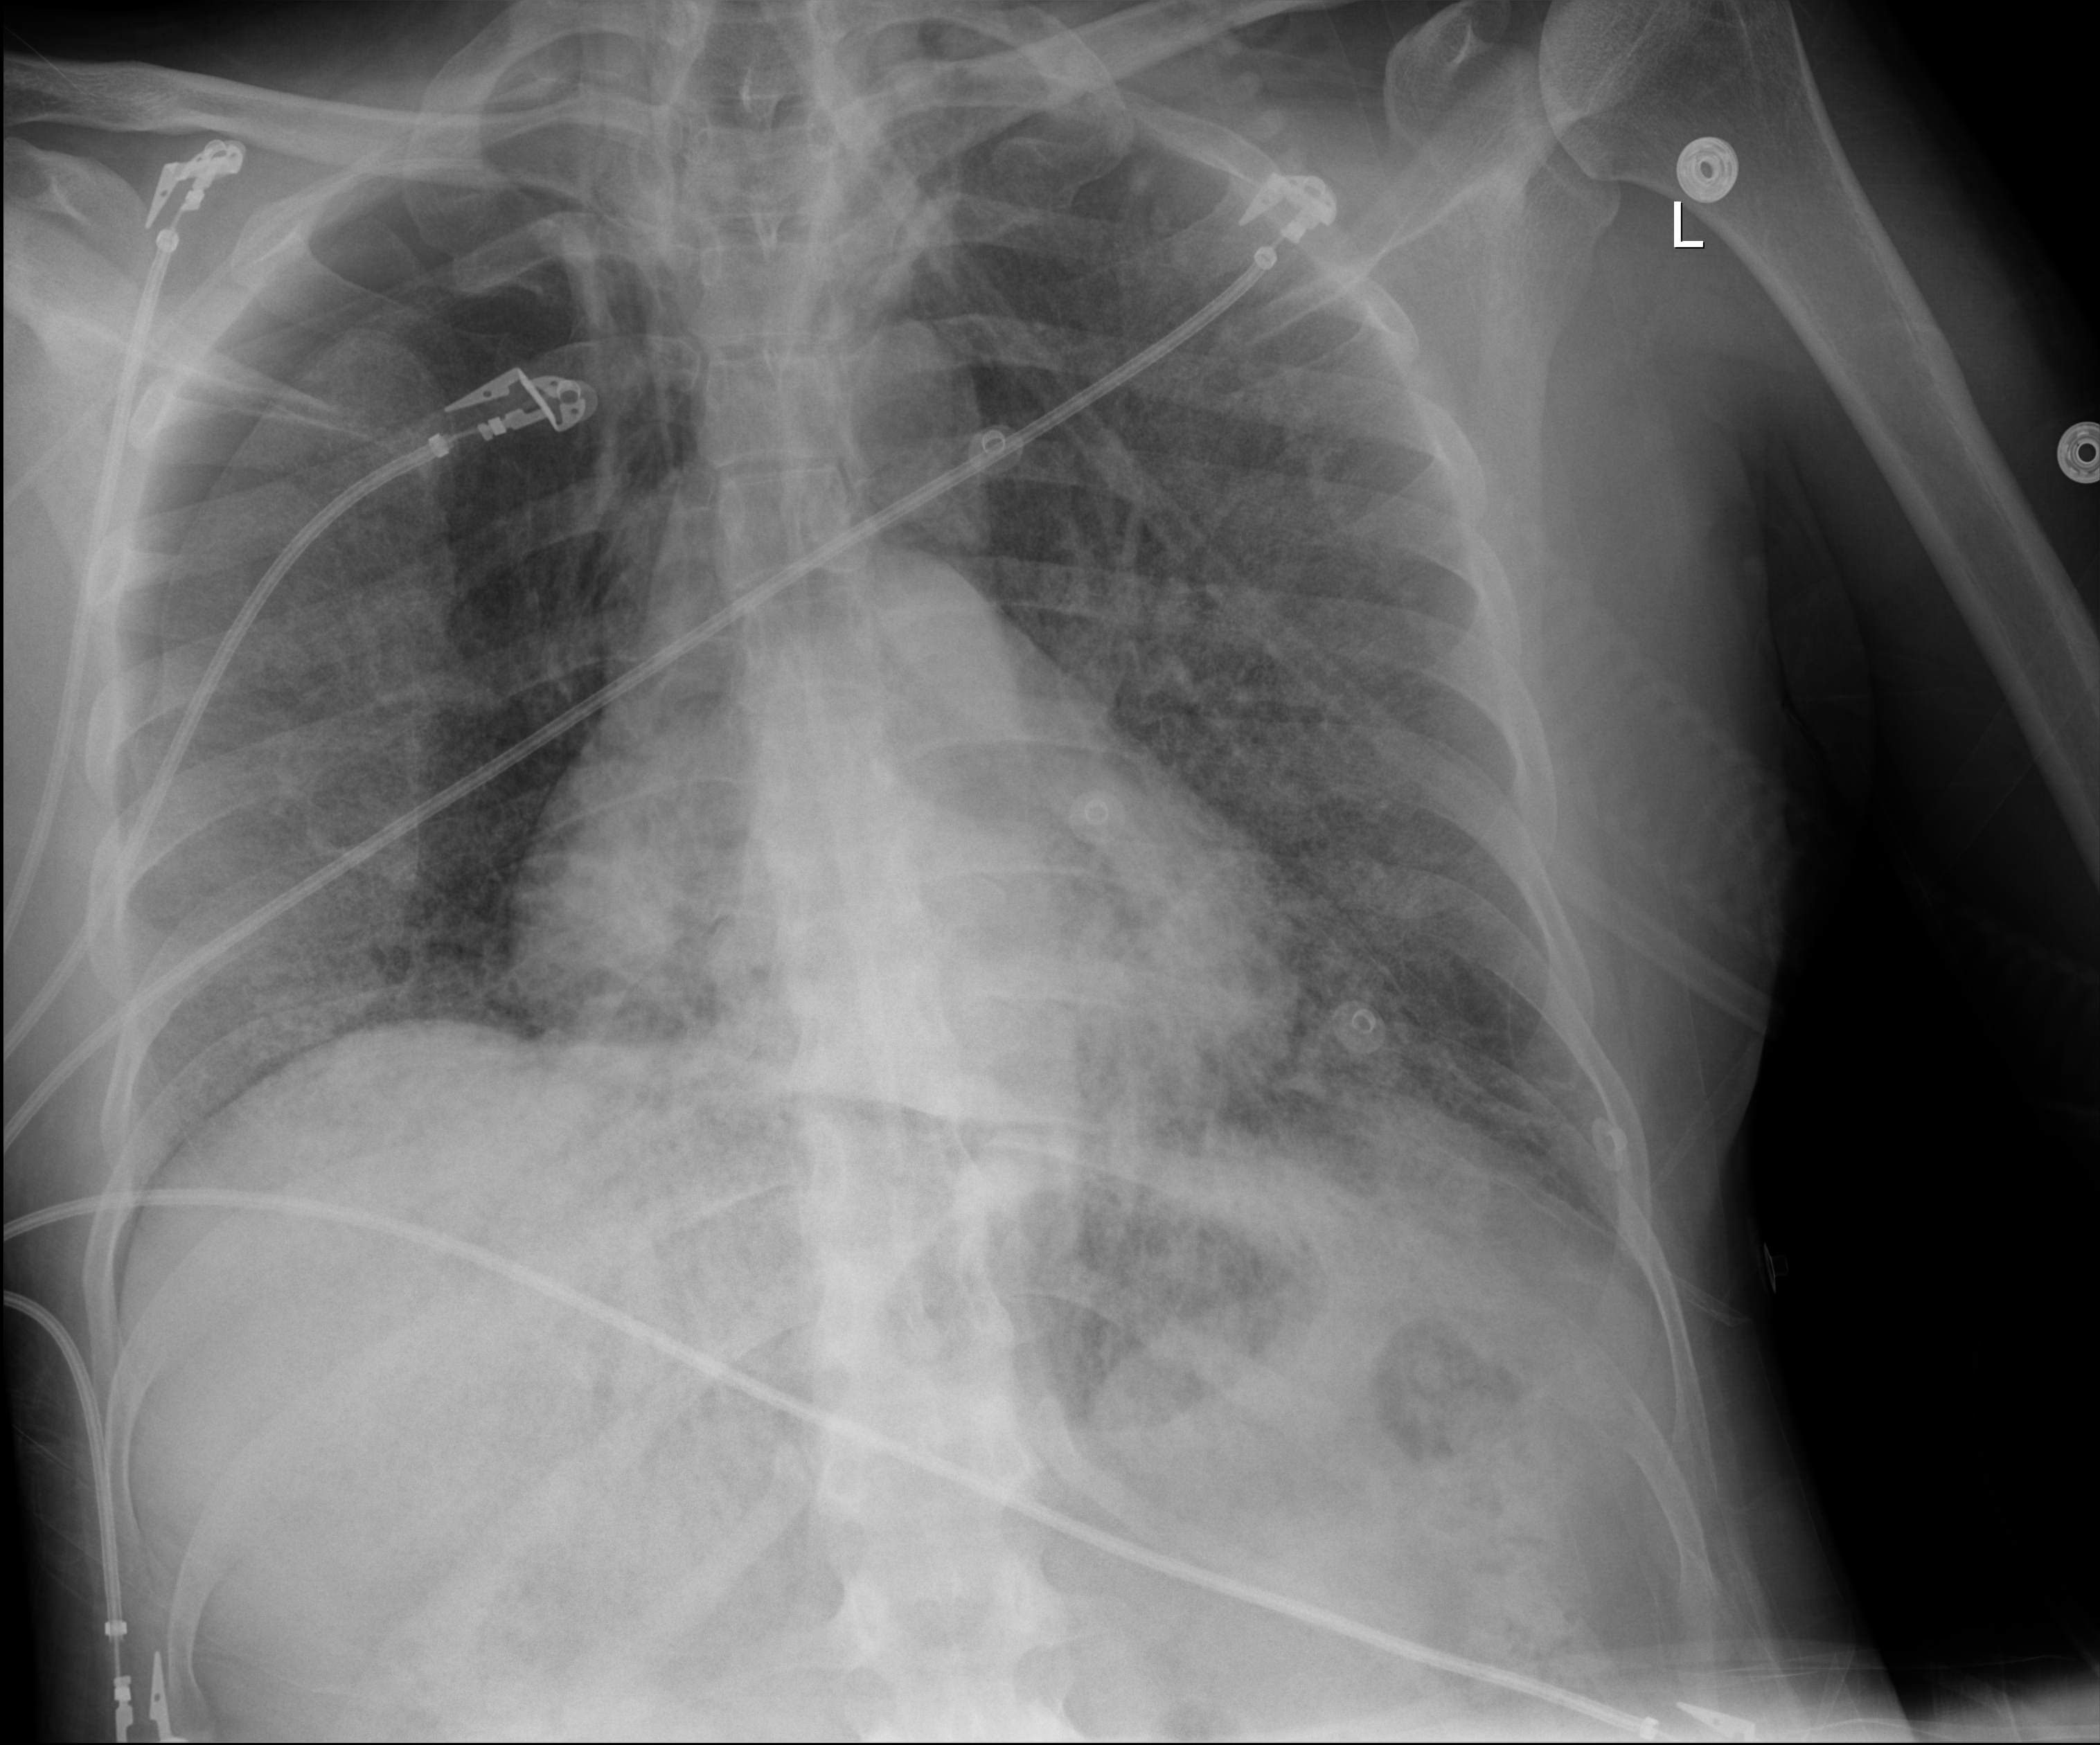
Chest X-ray (portable). Adult patient hospitalised with COVID-19, age 18–59 years.
Hospital-stay facts (about this admission, not read from this image; timing relative to this image not recorded): admitted to intensive care during this hospital stay: yes; other chronic lung disease (admission record): no; smoking status (admission record): never.